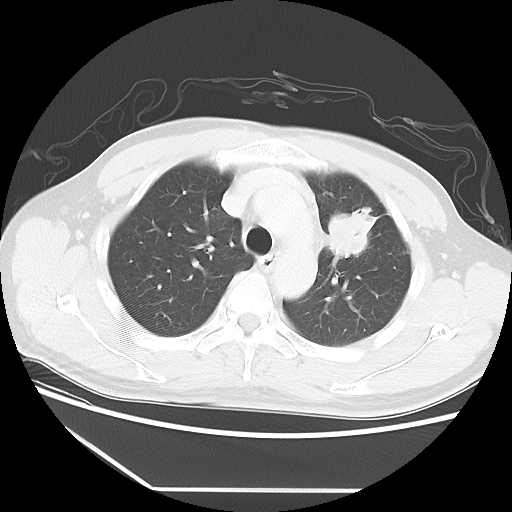
Chest CT, one axial slice. Reconstruction kernel LUNG. 120 kVp. Lung window (W 1500 / L -600 HU). 5 mm slice thickness. 512 × 512 image matrix. Patient: male, 53 years. From the clinical record (not read from this slice): clinical TNM (as recorded): T2a N1 M1b.
Outlined on this slice (rectangle marked by the reading radiologist):
- lung tumour (recorded histology: adenocarcinoma): box from (x=322, y=200) to (x=379, y=264) px